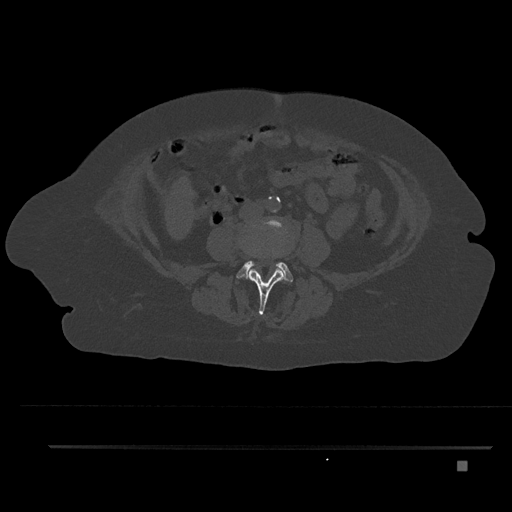
CT including the spine, one axial slice. Position 106 of 797 along the scan axis. Reconstruction kernel Br40s/3. Bone window (W 1800 / L 400 HU). 0.5 mm slice thickness. 512 × 512 image matrix, field of view 437 × 437 mm. Female patient, age 76 years. From the clinical record (not read from this slice): primary cancer: lung; vertebrae with lytic lesions (as recorded): T11, L3.
Annotated regions visible in this slice (semi-automatic segmentation, software-assisted and operator-edited):
- L3 vertebra: box from (x=249, y=249) to (x=285, y=314) px
- L4 vertebra: (x=237, y=221)–(x=293, y=282)